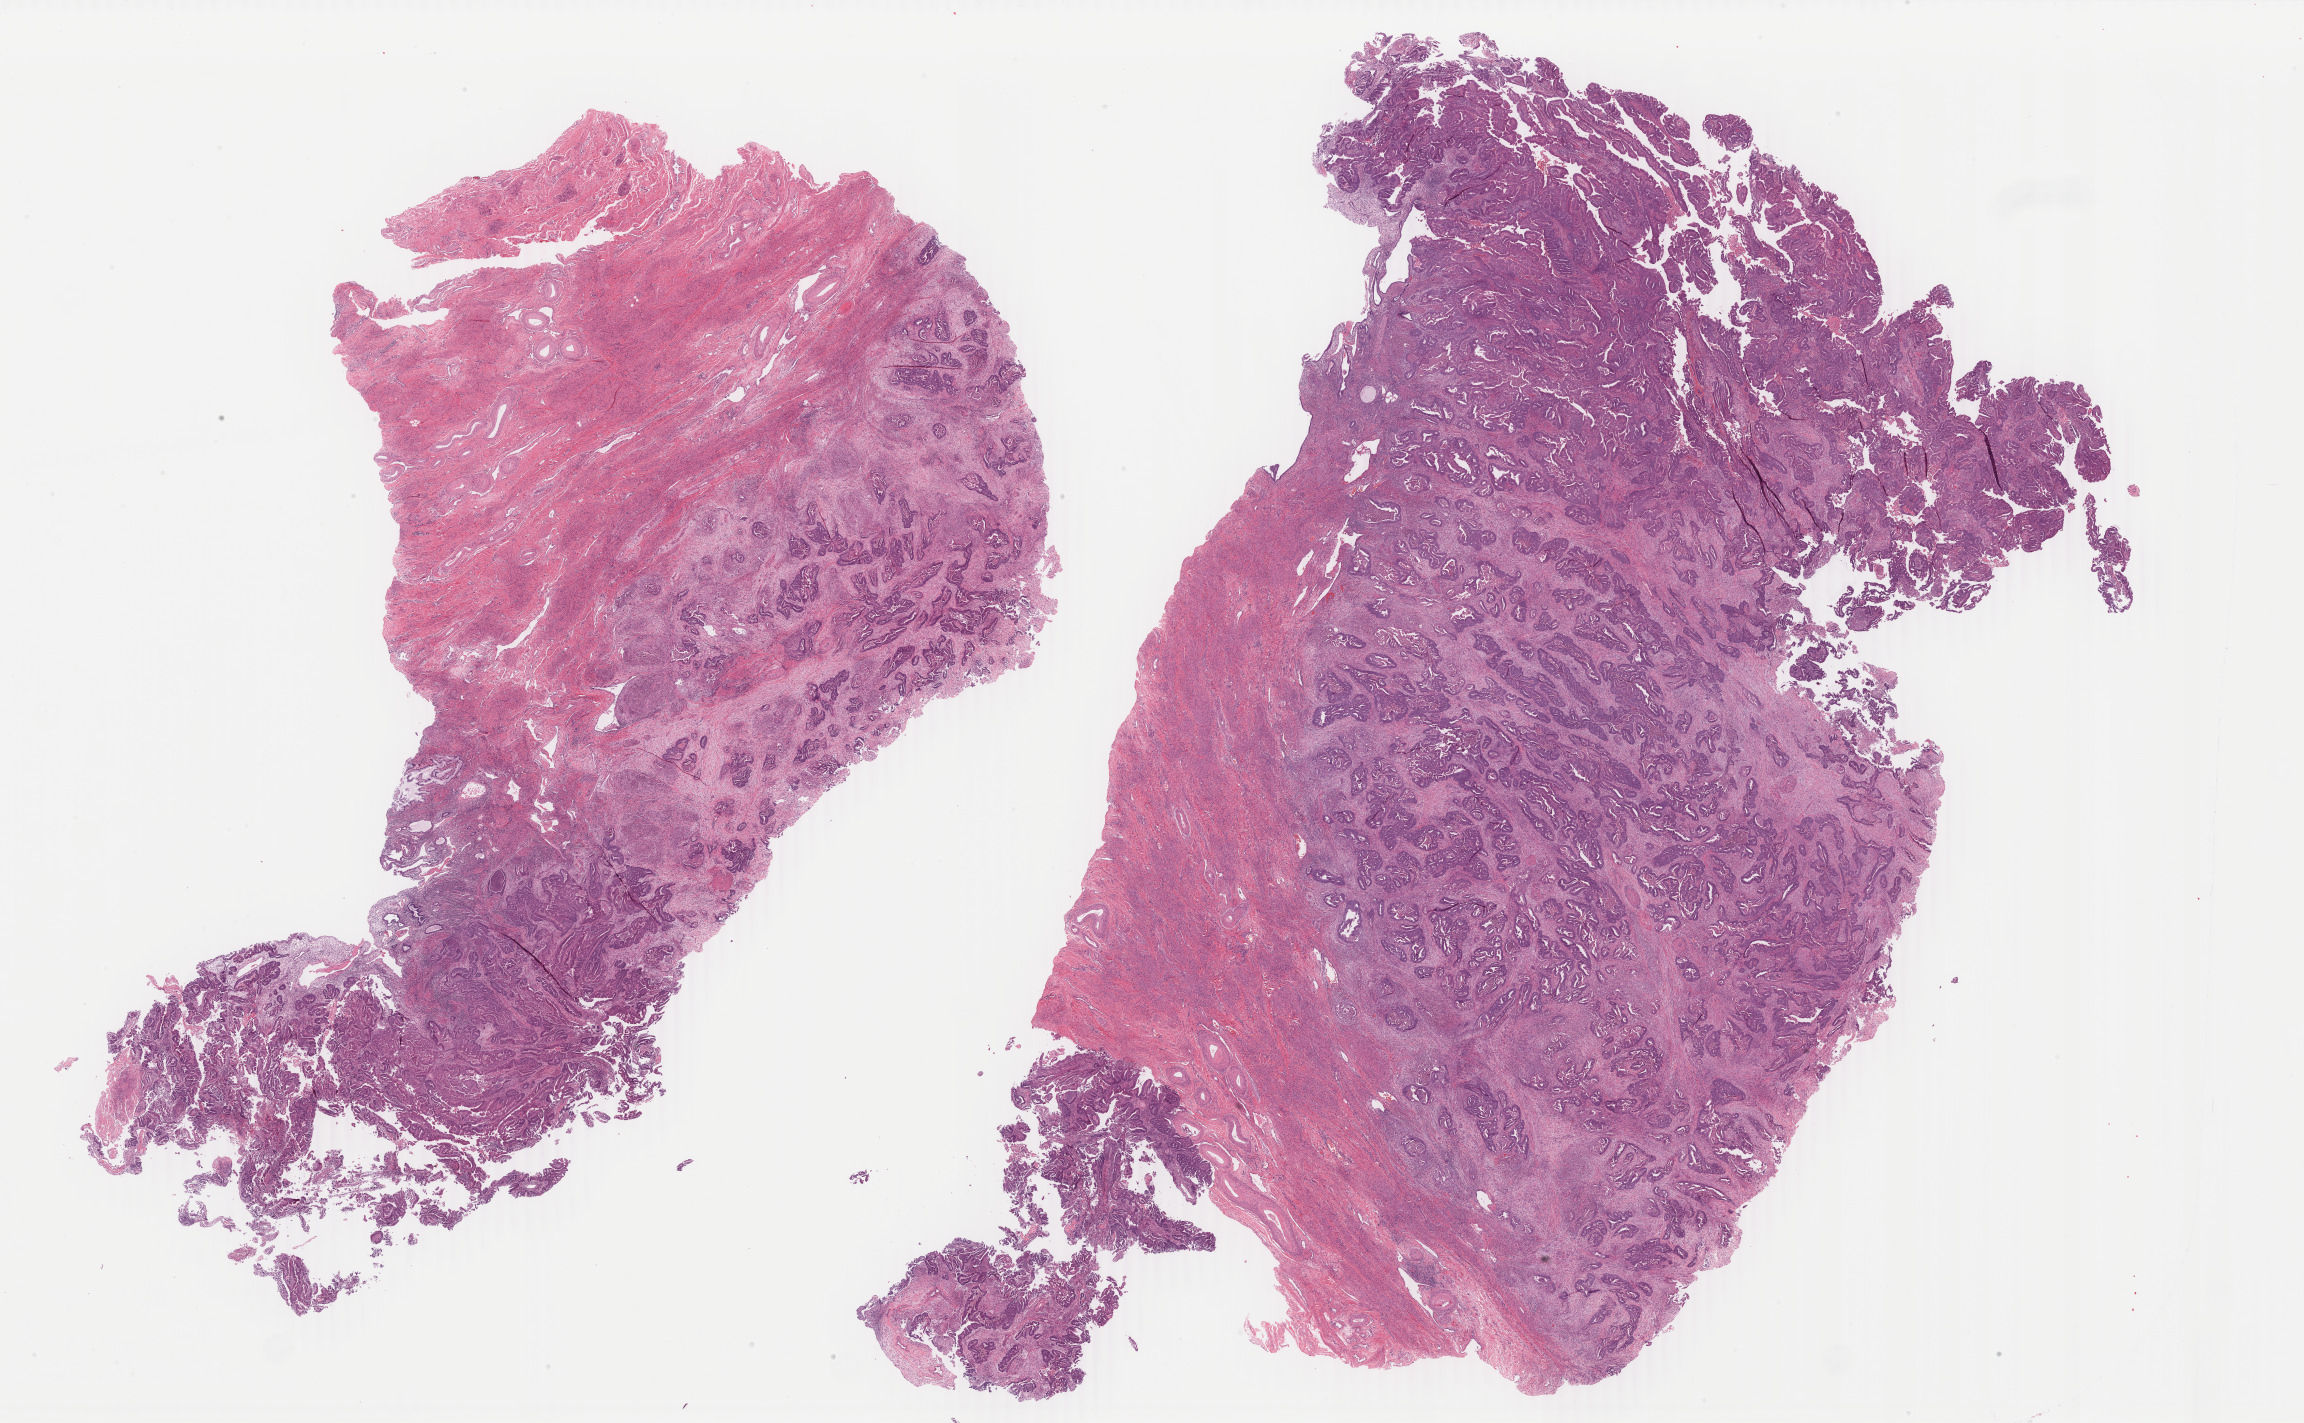
Digitized H&E tissue section (whole slide) — whole scanned area (about 36.6 x 22.6 mm, slide scanned at 40x) shown as a low-resolution overview. Formalin-fixed paraffin-embedded (FFPE) diagnostic section. Sample: primary tumour, uterus. Female patient; age at initial diagnosis 53 years. Histologic grade: G2 (moderately differentiated).
• FIGO stage: IIIC2
• lymph nodes positive (case pathology): 0 of 3 examined
• pathologic diagnosis: Endometrioid adenocarcinoma, NOS (endometrium)